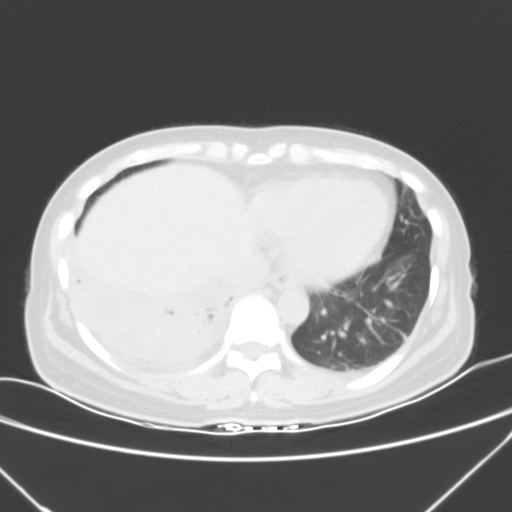
Chest CT, one axial slice; slice 12 of 53 in the series (ordered by position); 120 kVp; lung window (W 1500 / L -600 HU); 5 mm slice thickness; 512 × 512 image matrix, field of view 337 × 337 mm. Patient: female, 42 years. From the clinical record (not read from this slice): clinical TNM (as recorded): T3 N0 M1c.
Outlined on this slice (rectangle marked by the reading radiologist):
- lung tumour (recorded histology: adenocarcinoma): bounding box <66,273,215,374> (left, top, right, bottom; pixels)